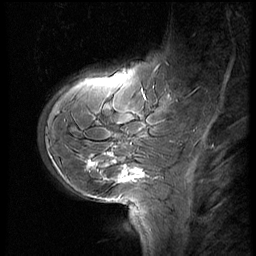
Breast MRI (dynamic contrast-enhanced), one sagittal slice; position 16 of 60 along the scan axis; 3 images stored at this slice position (order not interpretable as contrast timing); 1.5 T; TE 4.2 ms, TR 8.9 ms; 2.5 mm slice thickness; 256 × 256 image matrix, field of view 200 × 200 mm. Female patient, age 29 years. From the clinical record (not read from this slice): setting: breast cancer imaged before/during neoadjuvant chemotherapy.
Annotated regions visible in this slice (semi-automatic segmentation, software-assisted and operator-edited):
- analysis volume of interest (the breast-tissue region the enhancement analysis was run in; not a lesion): bounding box <40,57,185,200> (left, top, right, bottom; pixels)
- tumour enhancement mask (voxels above the 140 % enhancement threshold inside the analysis volume of interest): <89,162,145,183>